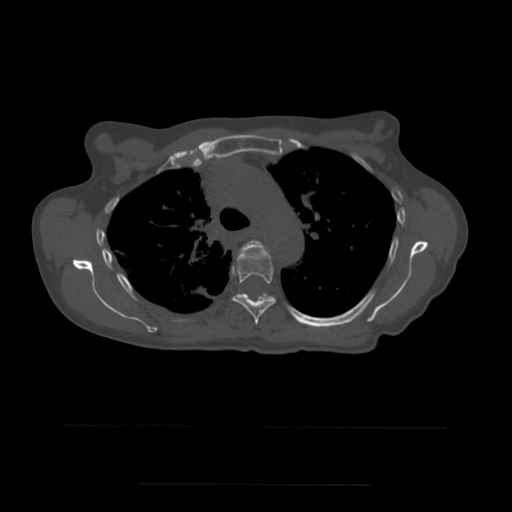
CT including the spine, one axial slice. Position 392 of 544 along the scan axis. Bone window (W 1800 / L 400 HU). 1.25 mm slice thickness. 512 × 512 image matrix, field of view 350 × 350 mm. Patient age 58 years. Case-level facts recorded for this patient, not image findings: primary cancer: lung.
Annotated regions visible in this slice (semi-automatically segmented with operator editing):
- T4 vertebra: box from (x=239, y=241) to (x=268, y=256) px
- T5 vertebra: (x=232, y=249)–(x=277, y=325)
- T6 vertebra: (x=240, y=294)–(x=270, y=300)